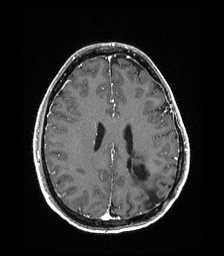
Brain MRI from a brain-tumour surgery series, one axial slice. Position 75 of 192 along the scan axis. T1-weighted post-contrast. 224 × 256 image matrix, field of view 224 × 256 mm. Case-level facts recorded for this patient, not image findings: histopathology: Low grade glioma; IDH mutation: no; tumour location: Left Parieto-Occipital Intraventricular.
Structures marked on this image (expert manual segmentation):
- previous resection cavity: bounding box [x1, y1, x2, y2] px = [133, 165, 162, 206]
- tumour: [131, 154, 143, 166]